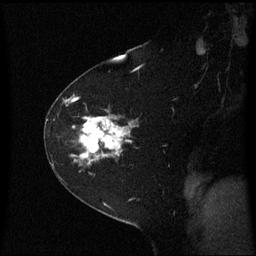
Breast MRI (dynamic contrast-enhanced), one sagittal slice; slice 43 of 60 in the series (ordered by position); dynamic contrast-enhanced series, image 2 of 3 at this slice position (ordered by acquisition); 1.5 T; TE 4.2 ms, TR 8.4 ms; 2 mm slice thickness; 256 × 256 image matrix, field of view 210 × 210 mm. Female patient, age 60 years. Case-level facts recorded for this patient, not image findings: setting: breast cancer imaged before/during neoadjuvant chemotherapy; receptor status: triple-negative.
Outlined on this slice (semi-automatic segmentation, software-assisted and operator-edited):
- analysis volume of interest (the breast-tissue region the enhancement analysis was run in; not a lesion): bounding box <46,99,142,182> (left, top, right, bottom; pixels)
- tumour enhancement mask (voxels above the 70 % enhancement threshold inside the analysis volume of interest): <65,99,134,166>